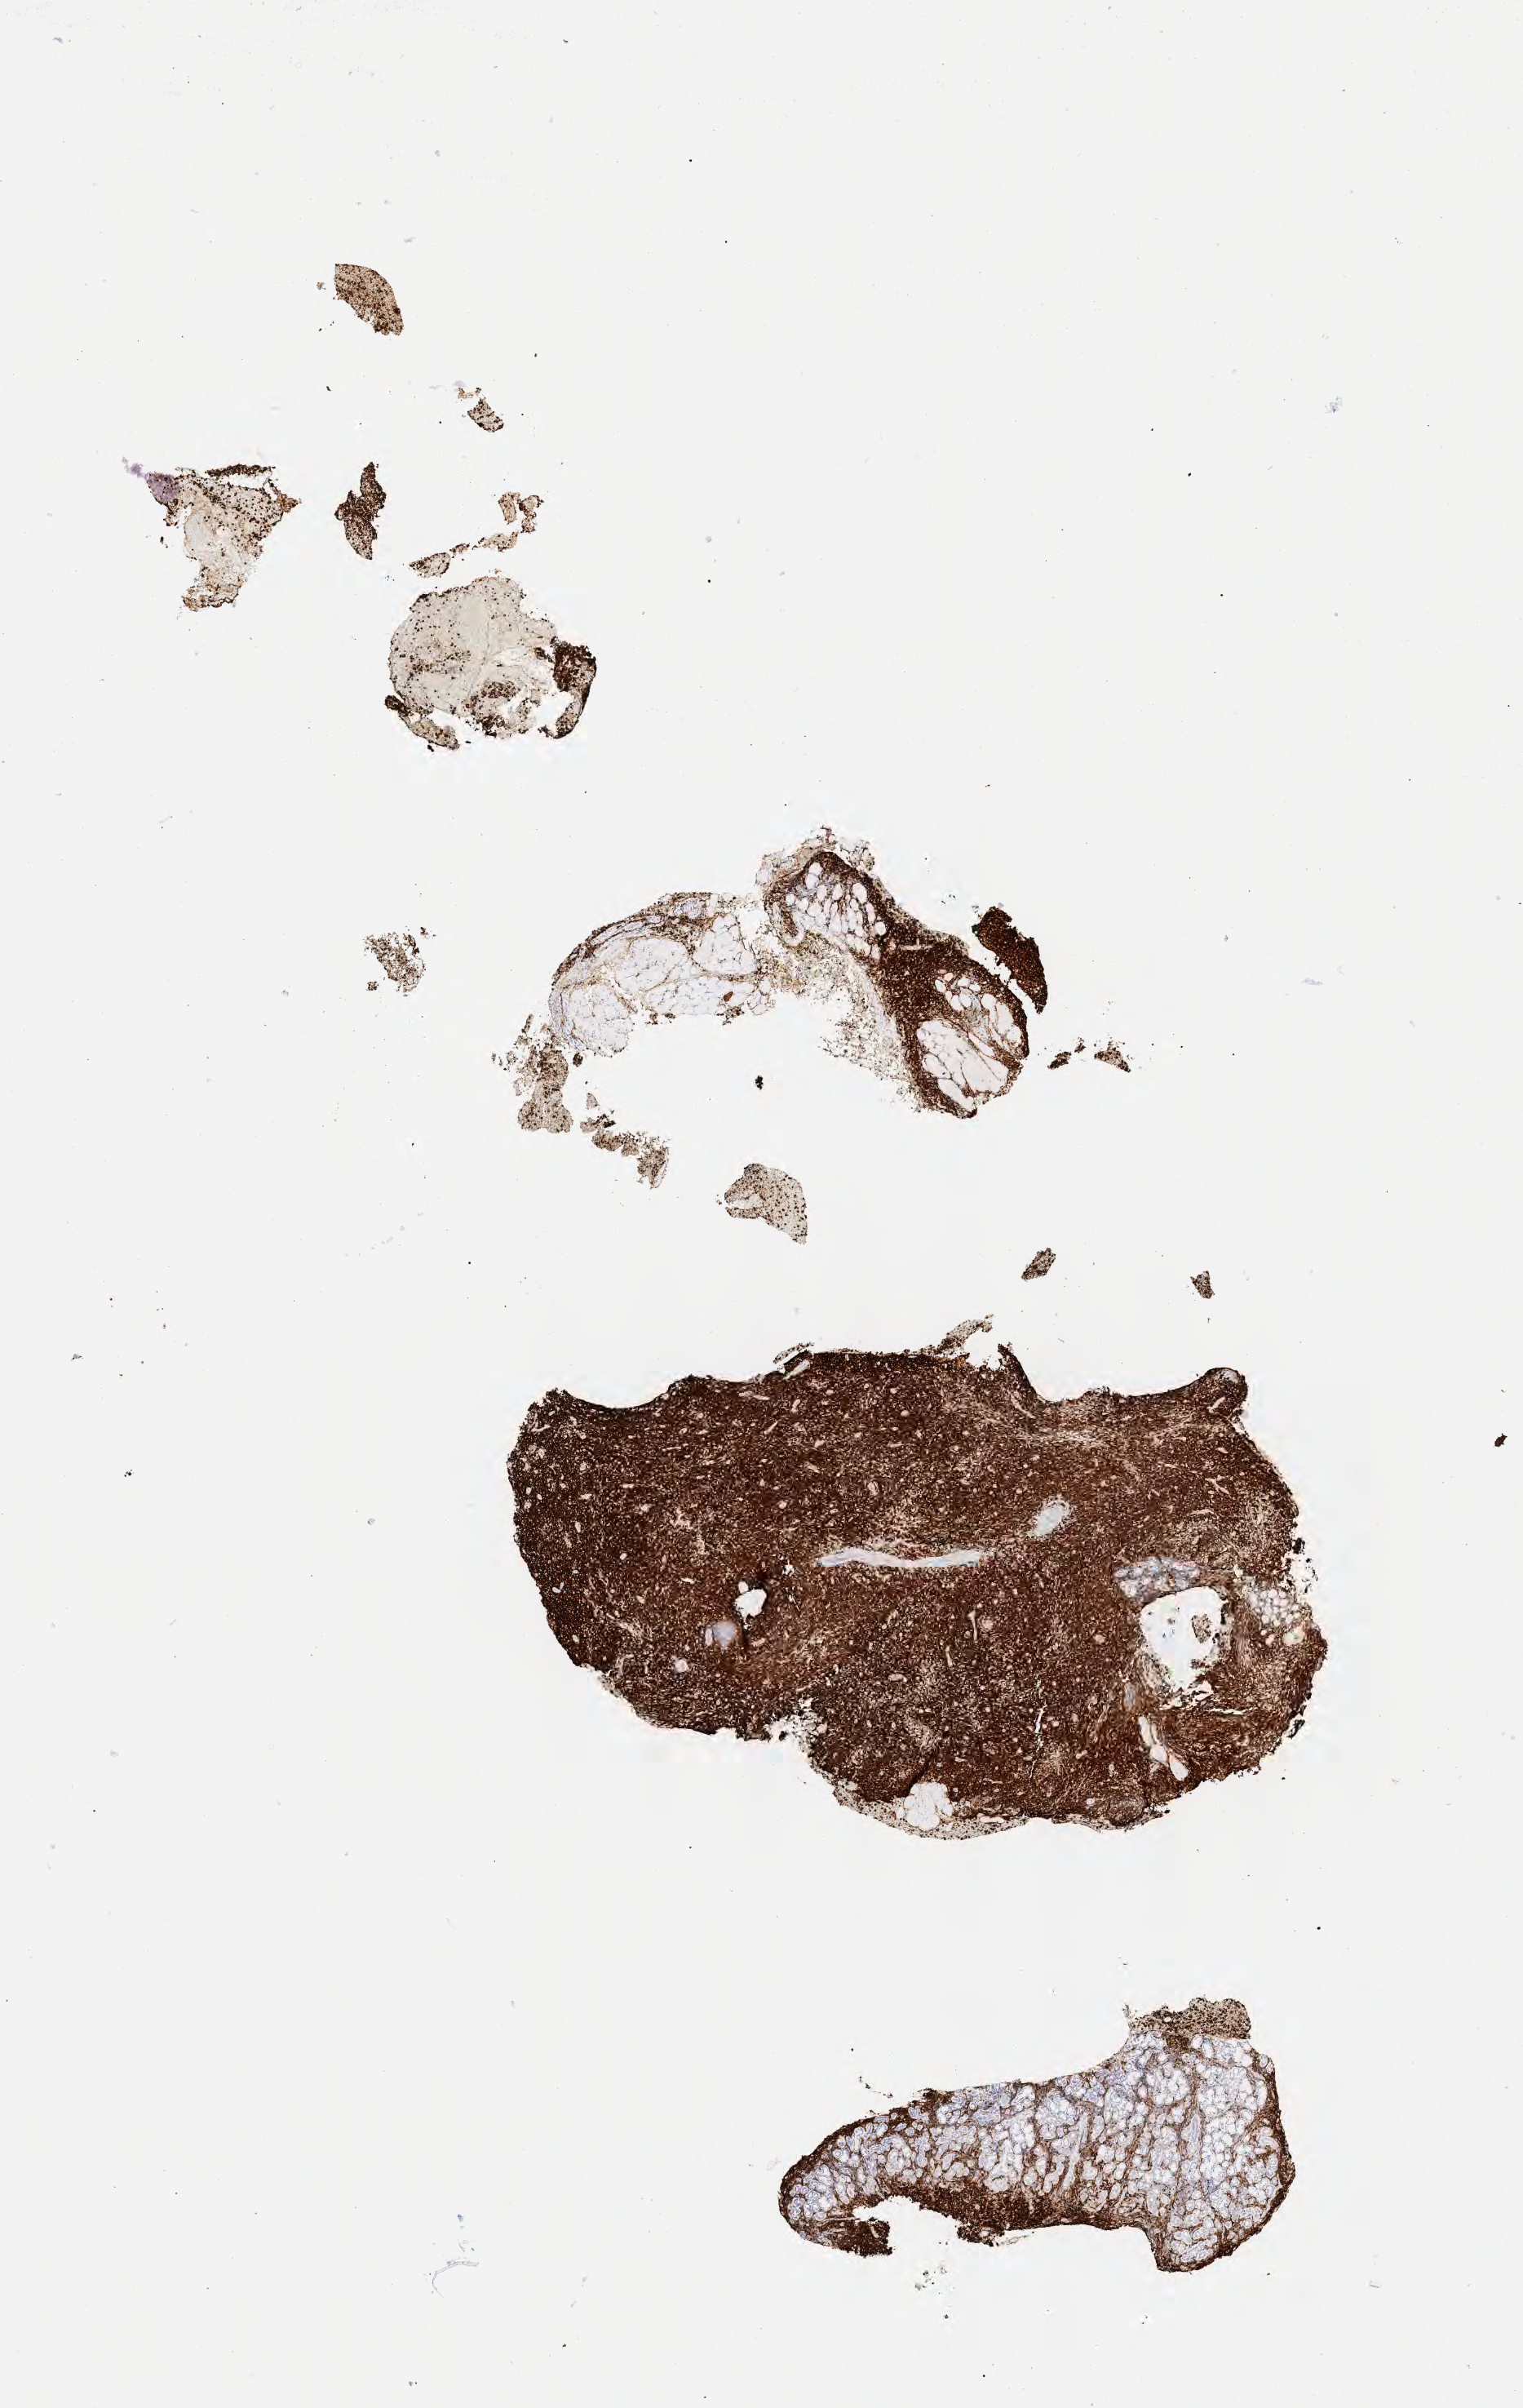
Immunohistochemistry (IHC) whole-slide image stained for CD79a, low-resolution overview of the scanned area, about 7.5 x 11.9 mm; tumor tissue. Male patient, age 53 years.
Diagnosis: Diffuse large B-cell lymphoma, NOS.